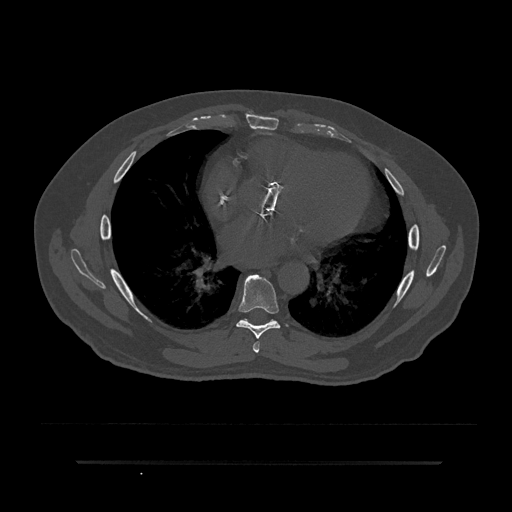
CT including the spine, one axial slice. Slice 473 of 797 in the series (ordered by position). Reconstruction kernel Br40s/3. 120 kVp. Bone window (W 1800 / L 400 HU). 0.5 mm slice thickness. 512 × 512 image matrix, field of view 464 × 464 mm. Patient: male, 59 years. From the clinical record (not read from this slice): primary cancer: bile ducts.
Outlined on this slice (semi-automatically segmented with operator editing):
- T6 vertebra: bounding box [x1, y1, x2, y2] px = [253, 342, 260, 353]
- T7 vertebra: [236, 274, 280, 339]
- T8 vertebra: [242, 319, 247, 321]